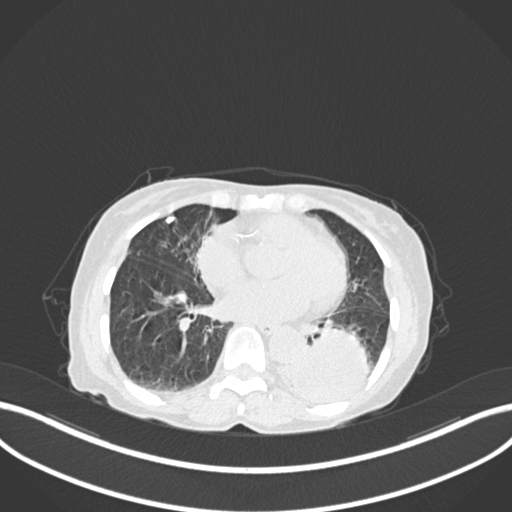
Chest CT, one axial slice. Position 54 of 233 along the scan axis. Reconstruction kernel B30f. 120 kVp. Lung window (W 1500 / L -600 HU). 1 mm slice thickness. 512 × 512 image matrix. Female patient, age 78 years. From the clinical record (not read from this slice): clinical TNM (as recorded): T3 N0 M1.
Annotated regions visible in this slice (bounding box drawn by a radiologist):
- lung tumour (recorded histology: squamous cell carcinoma): box from (x=278, y=311) to (x=375, y=407) px